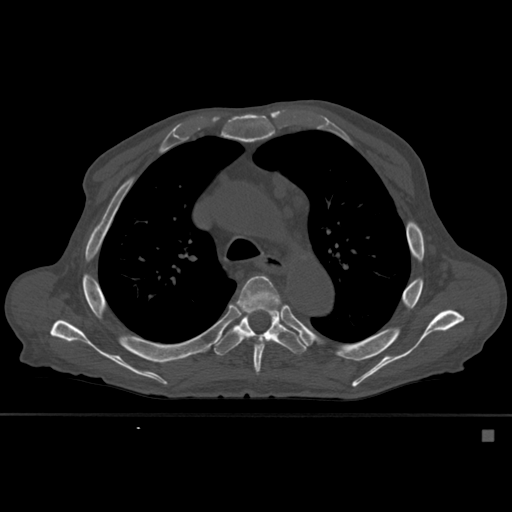
CT including the spine, one axial slice. Bone window (W 1800 / L 400 HU). 1.5 mm slice thickness. 512 × 512 image matrix, field of view 373 × 373 mm. Male patient, age 78 years. Case-level facts recorded for this patient, not image findings: primary cancer: prostate.
Annotated regions visible in this slice (semi-automatic segmentation, software-assisted and operator-edited):
- T5 vertebra: bounding box (x1, y1, x2, y2) in pixels: (236, 275, 281, 376)
- T6 vertebra: (213, 308, 306, 356)